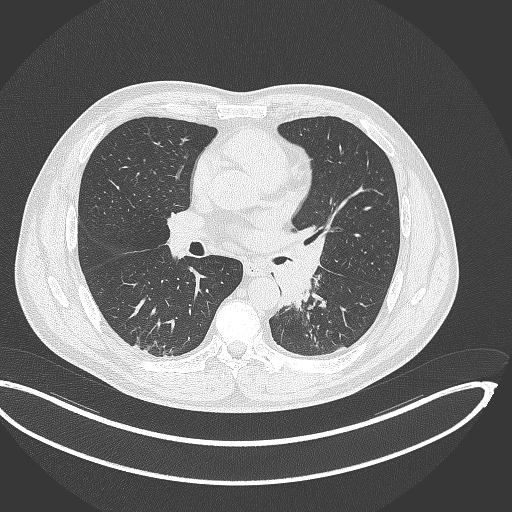
Chest CT, one axial slice; slice 189 of 362 in the series (ordered by position); reconstruction kernel B70f; lung window (W 1500 / L -600 HU); 1 mm slice thickness; 512 × 512 image matrix, field of view 442 × 442 mm. Patient: male, 50 years. From the clinical record (not read from this slice): clinical TNM (as recorded): T2a N3 M0.
Annotated regions visible in this slice (bounding box drawn by a radiologist):
- lung tumour (recorded histology: squamous cell carcinoma): box from (x=270, y=234) to (x=327, y=308) px